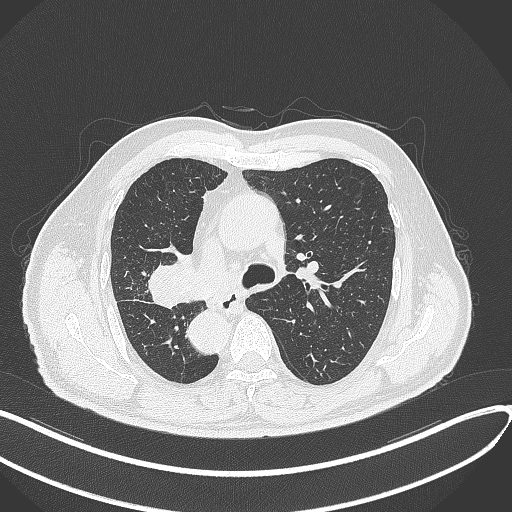
Chest CT, one axial slice. Position 200 of 300 along the scan axis. Reconstruction kernel B70f. 120 kVp. Lung window (W 1500 / L -600 HU). 512 × 512 image matrix. Male patient, age 67 years. Case-level facts recorded for this patient, not image findings: clinical TNM (as recorded): T2a N0 M0.
Annotated regions visible in this slice (bounding box drawn by a radiologist):
- lung tumour (recorded histology: squamous cell carcinoma): bounding box [x1, y1, x2, y2] px = [143, 256, 196, 311]